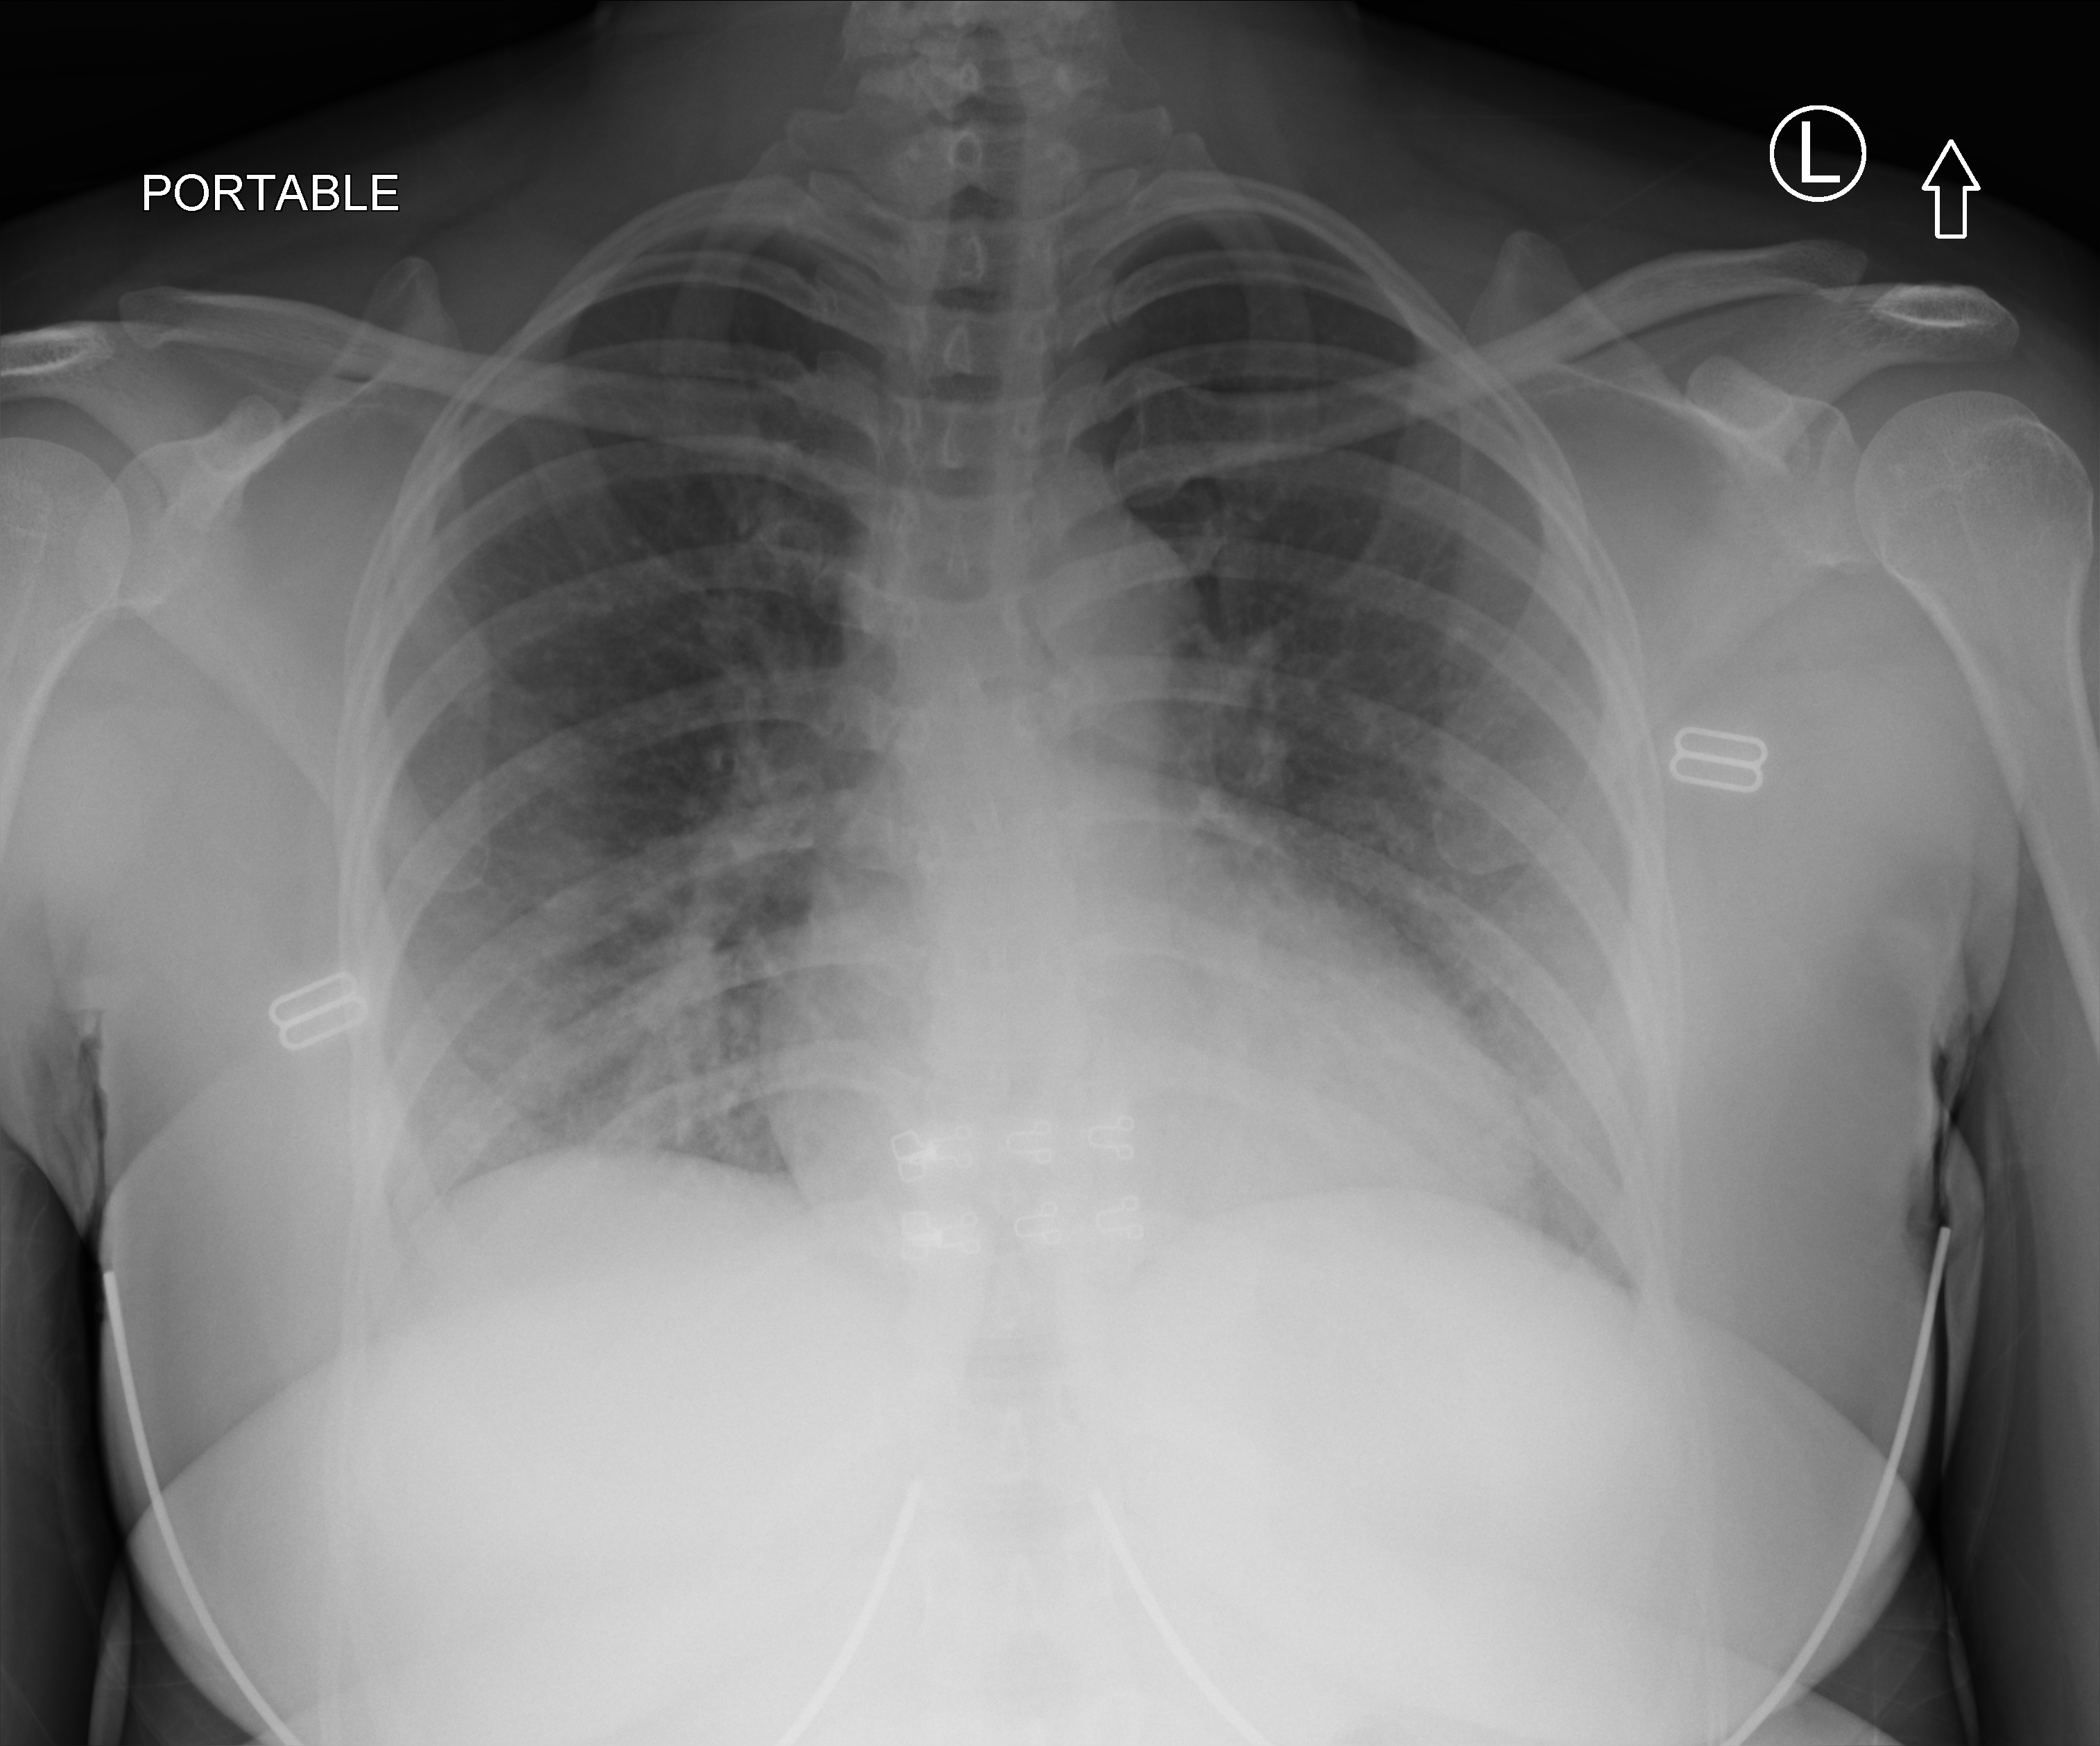
Bedside chest radiograph (computed radiography). Female patient hospitalised with COVID-19, age 18–59 years.
From the hospital-stay record, not from the radiograph (when in the stay this image was taken is not recorded): admitted to intensive care during this hospital stay: no.